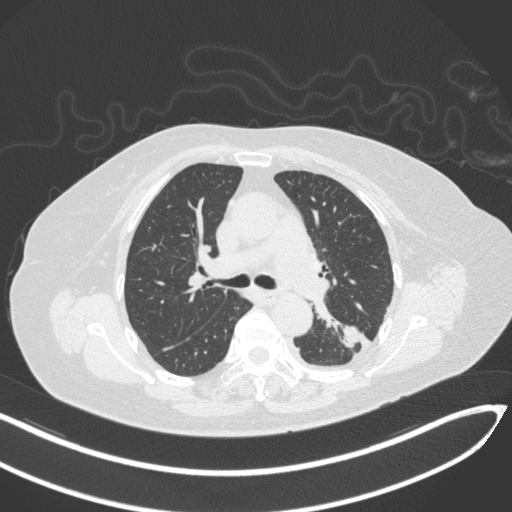
Chest CT, one axial slice. Position 201 of 270 along the scan axis. Lung window (W 1500 / L -600 HU). 1 mm slice thickness. 512 × 512 image matrix. Patient: female, 76 years. From the clinical record (not read from this slice): clinical TNM (as recorded): T1c N0 M0.
Annotated regions visible in this slice (rectangle marked by the reading radiologist):
- lung tumour (recorded histology: adenocarcinoma): bounding box (x1, y1, x2, y2) in pixels: (337, 320, 365, 352)